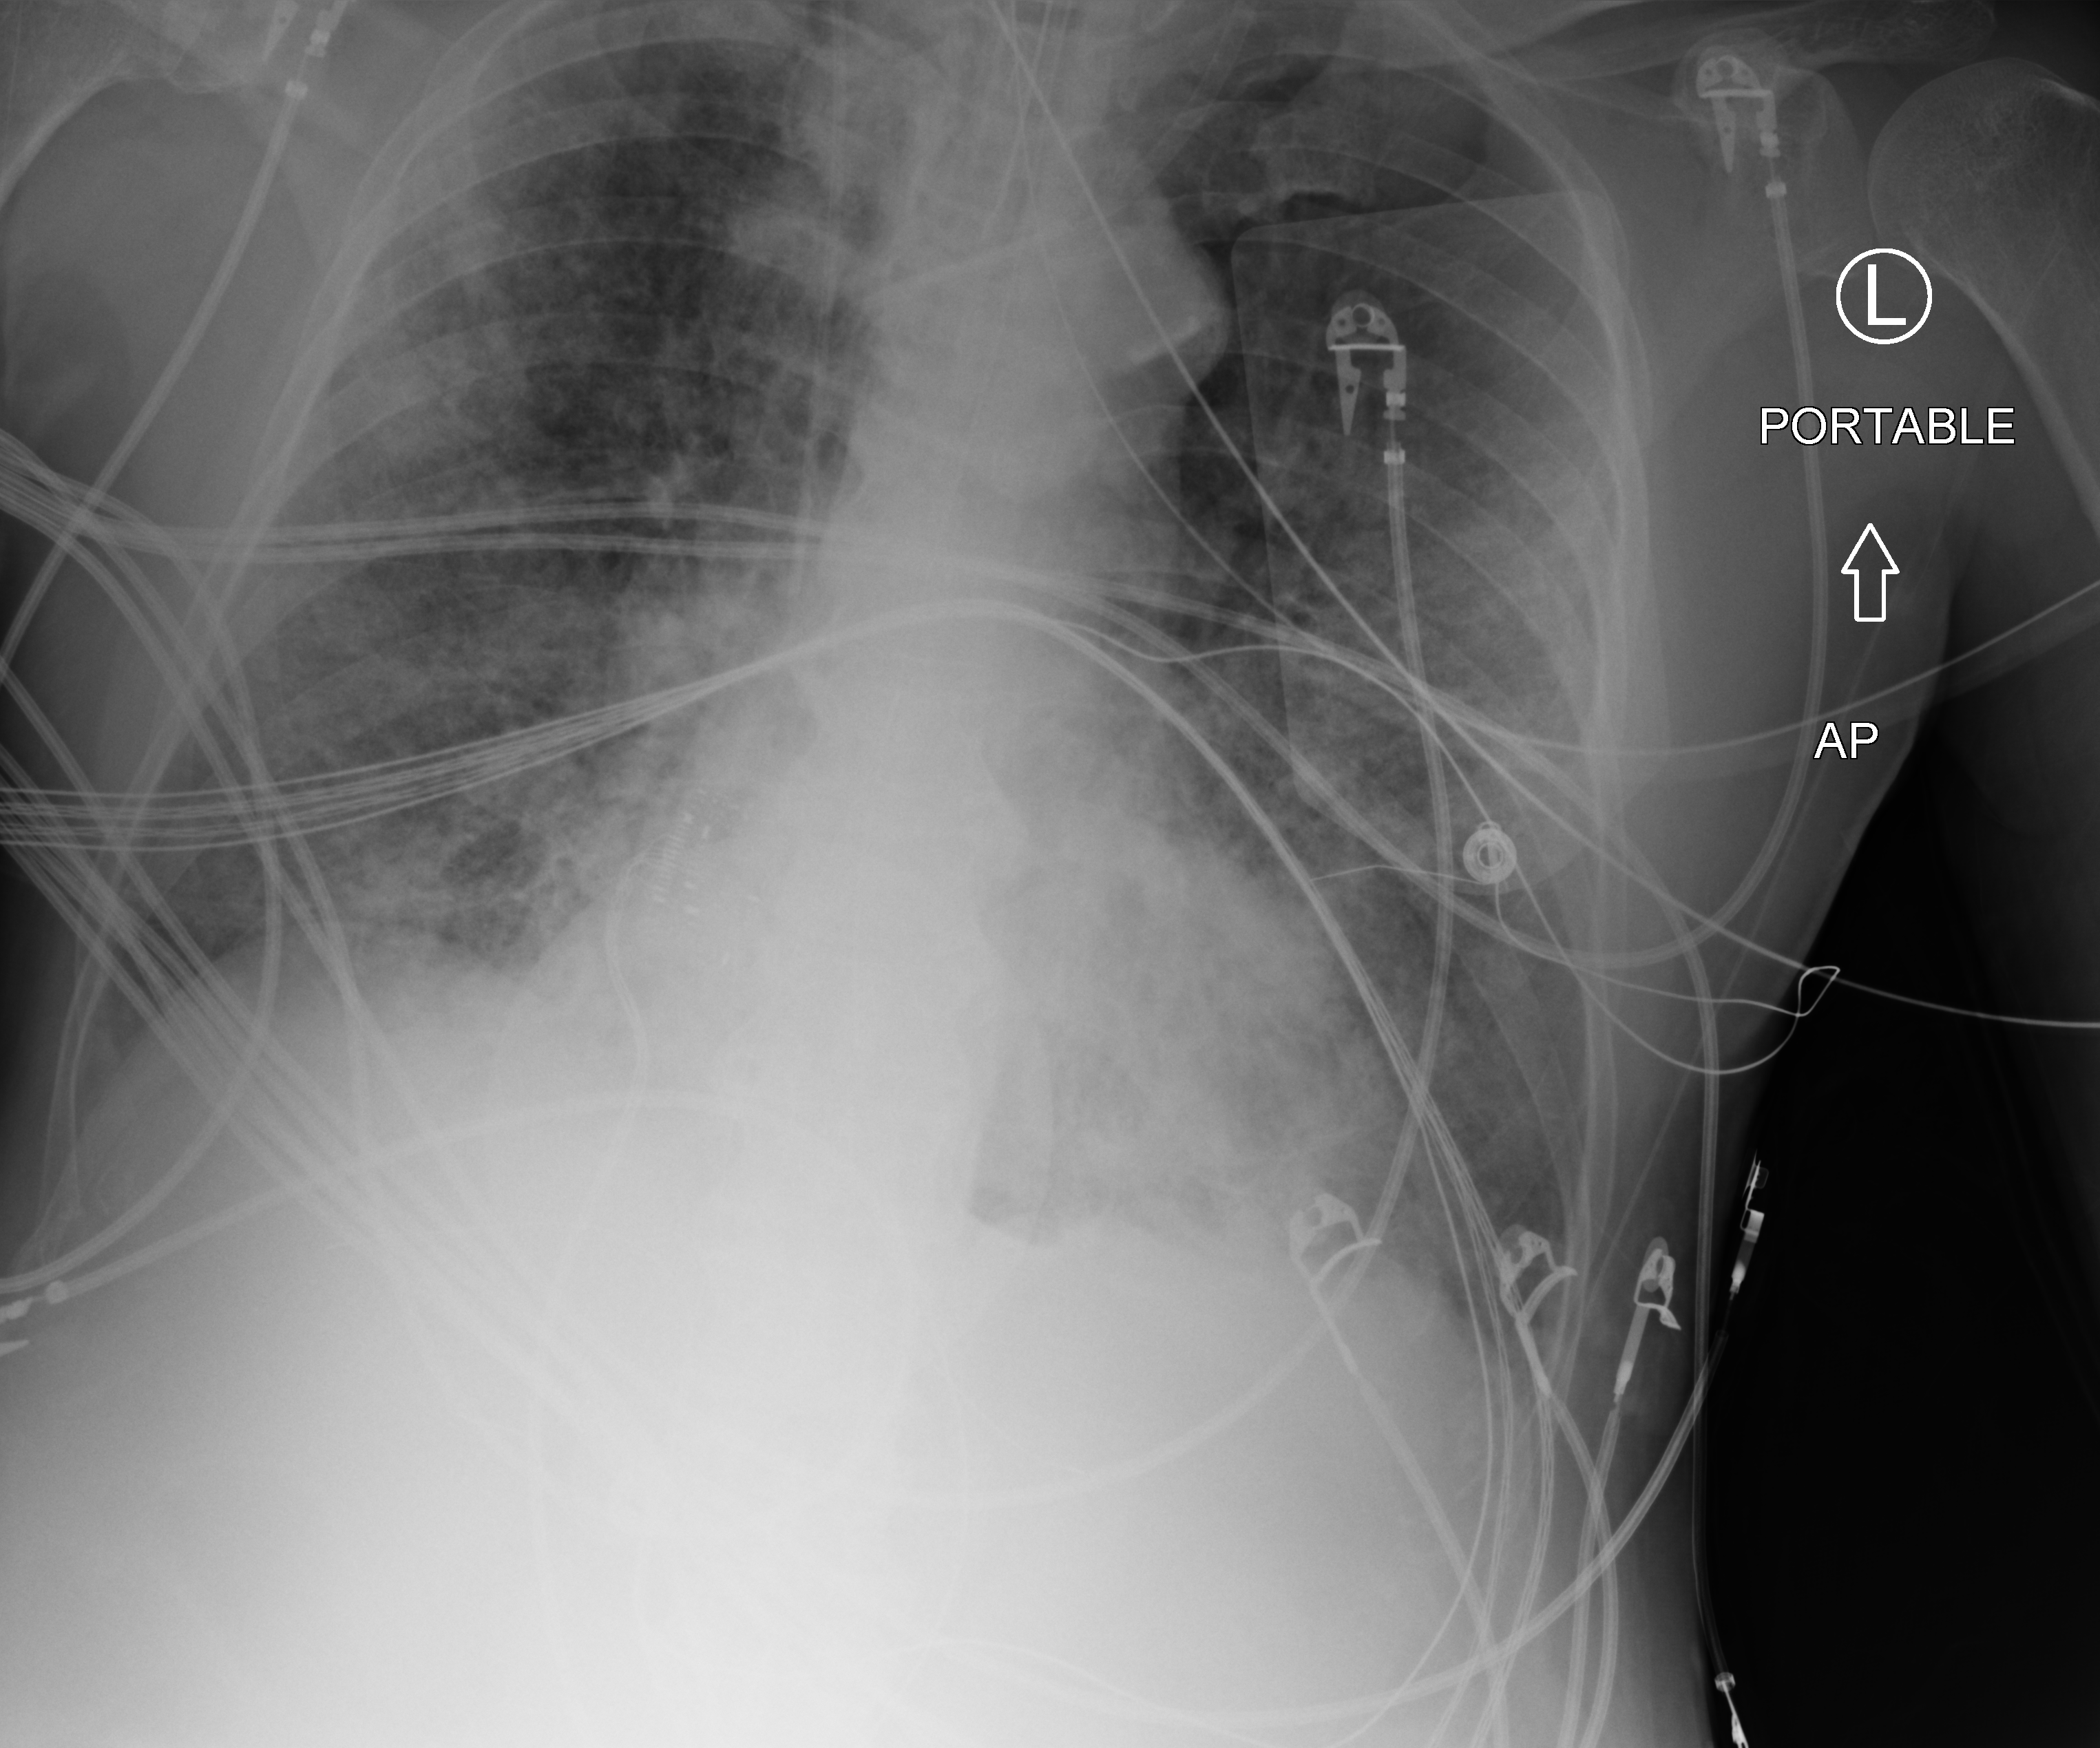
Bedside chest radiograph (computed radiography); anteroposterior (AP) projection. Male patient hospitalised with COVID-19, age 60–74 years.
From the hospital-stay record, not from the radiograph (when in the stay this image was taken is not recorded):
- length of hospital stay: 26 days
- admitted to intensive care during this hospital stay: yes
- mechanically ventilated during this hospital stay: yes